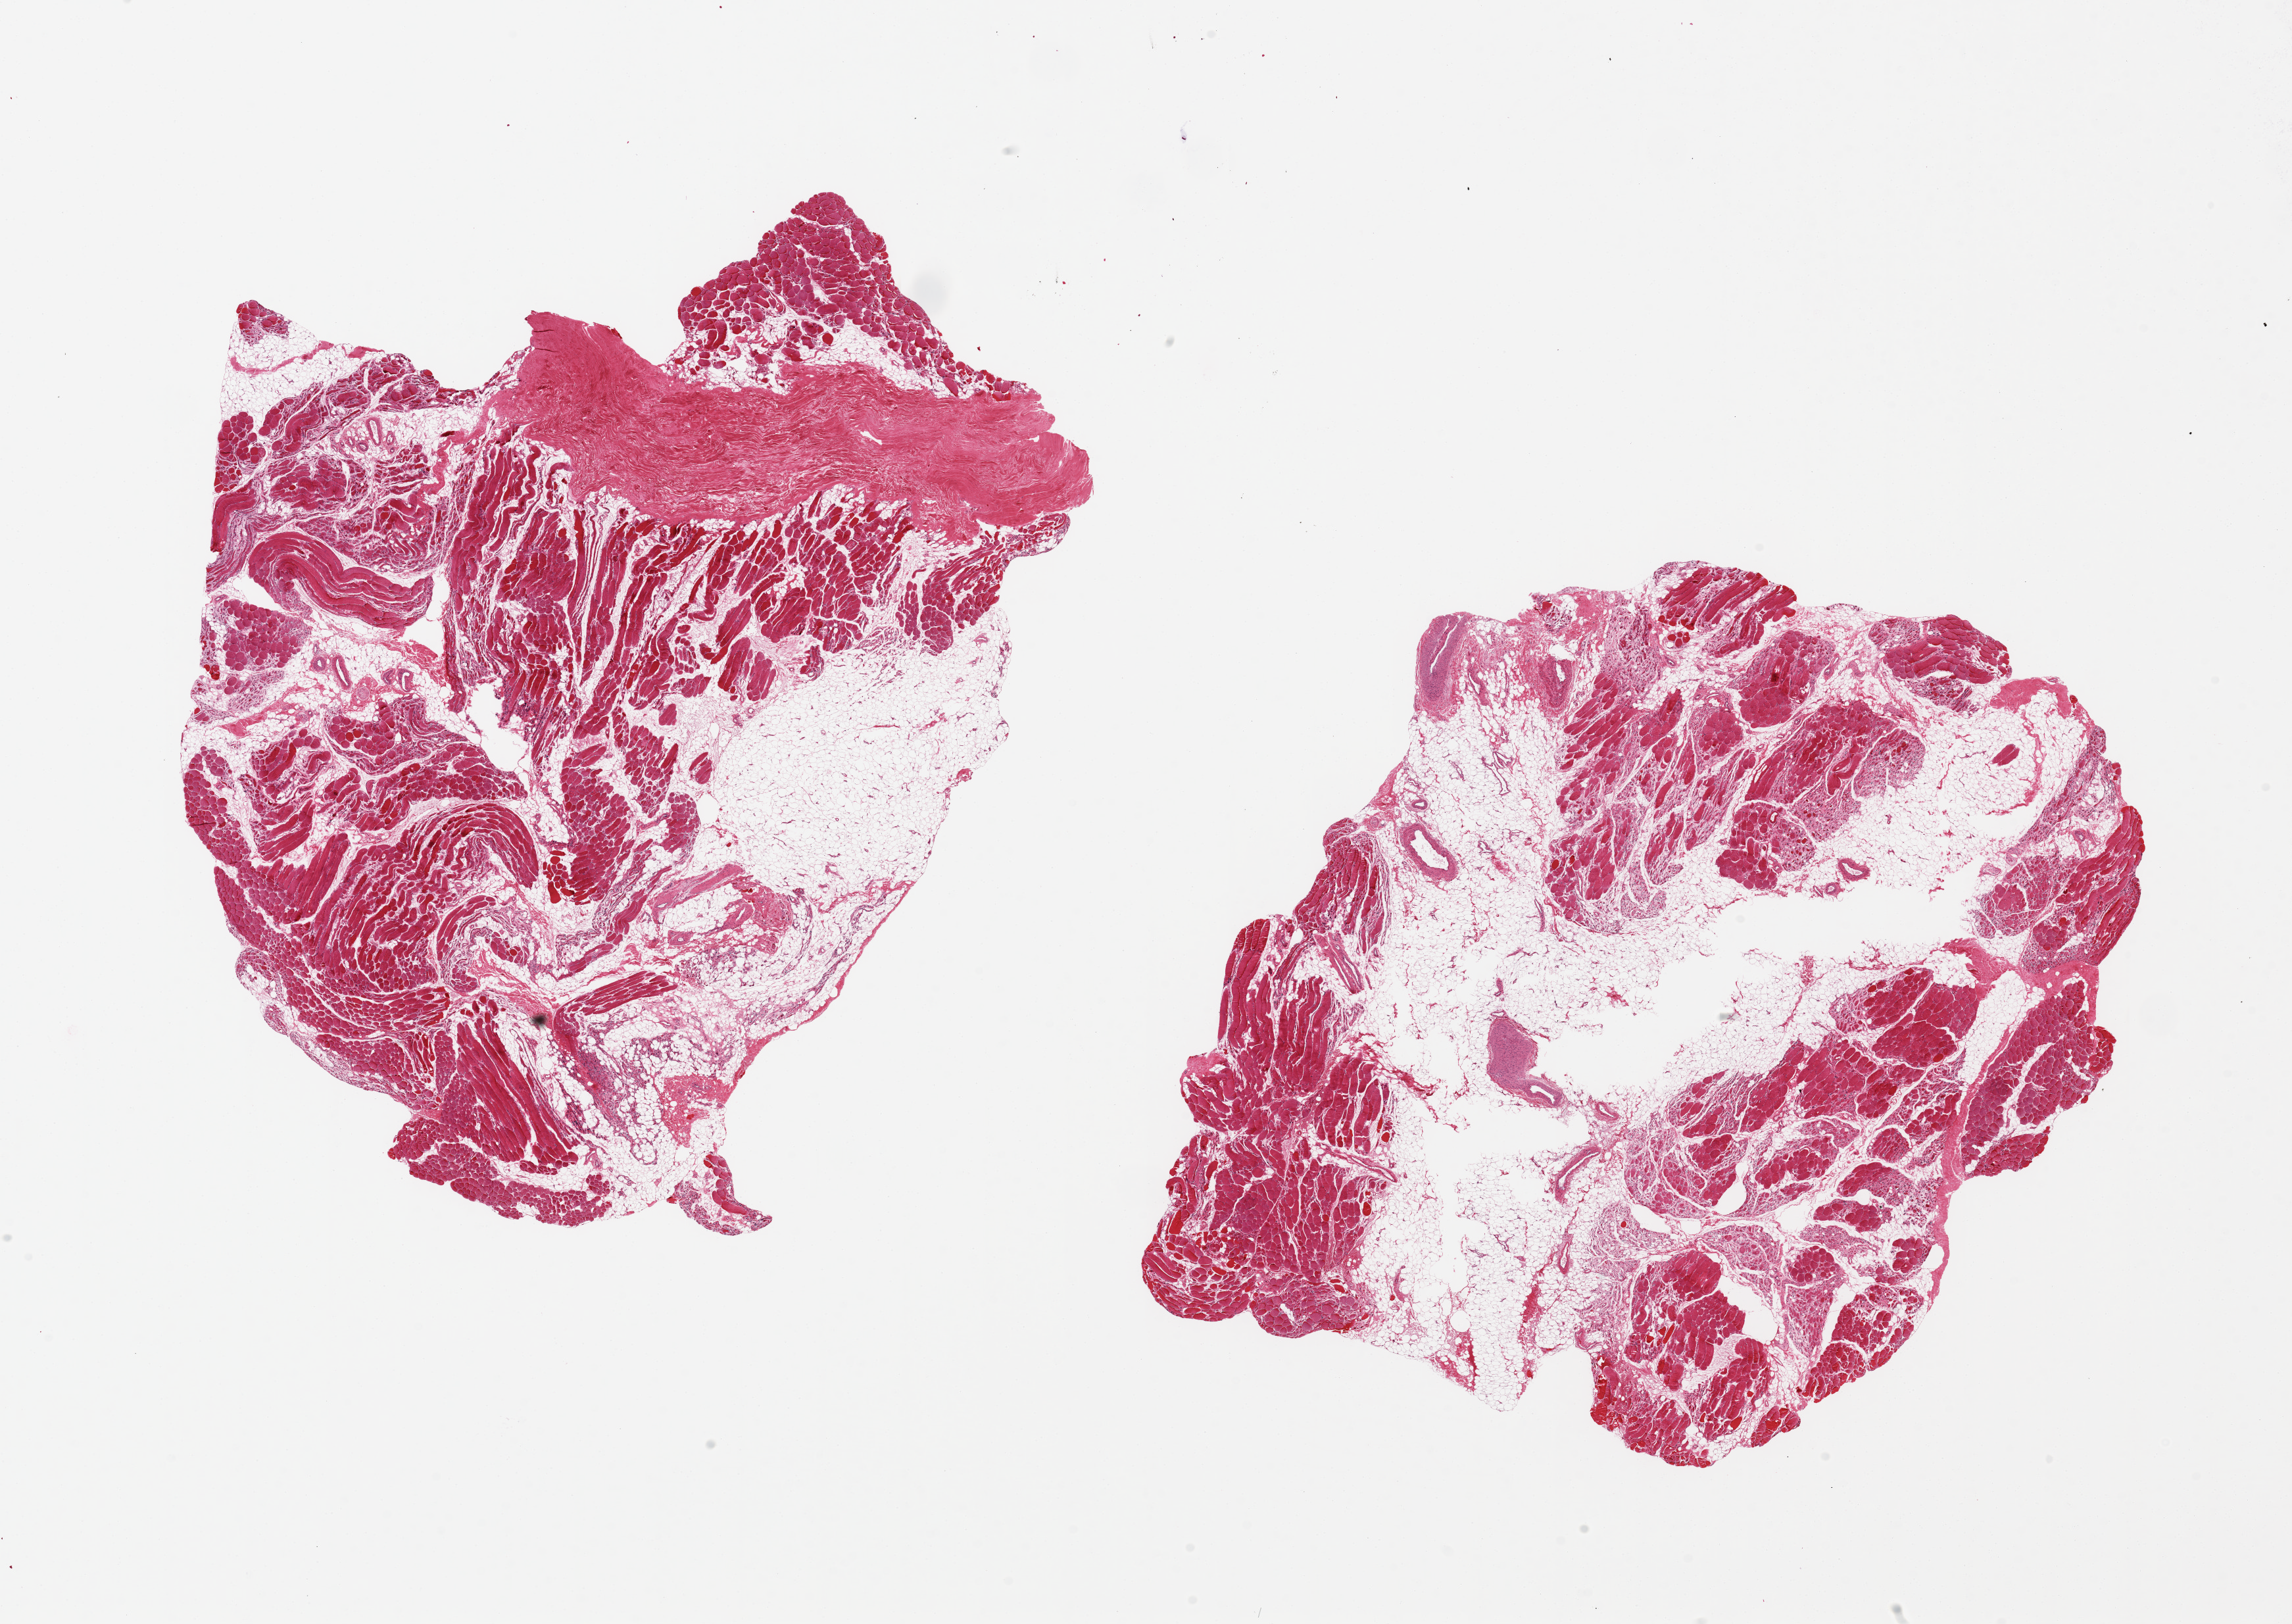
Digitized H&E-stained section, whole scanned area (about 27.6 x 19.5 mm, from a 20x scan) shown as a low-resolution overview, PAXgene-fixed paraffin-embedded (PFPE) section, section of skeletal muscle (target tissue), tissue donor sample. Donor sex: male.
* review note (as recorded): 2 pieces, ~12x10mm. ~40-50% interstitial fat, mildly atrophic-appearing skeletal muscle fibers